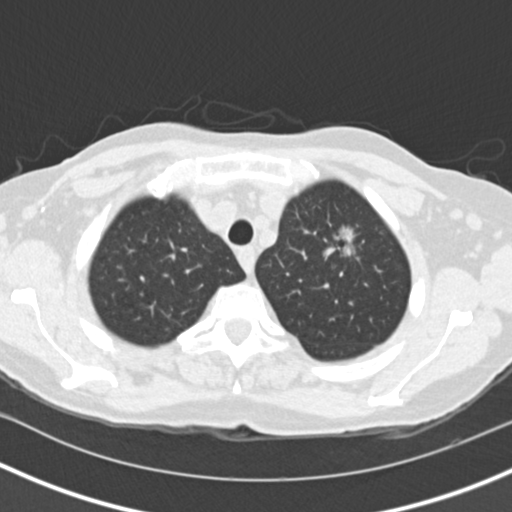
Low-dose screening chest CT, axial slice; first (baseline) screen; lung window (W 1500 / L -600 HU); 2 mm slice thickness; standard (soft-tissue) reconstruction kernel (B30f); slice 25 of 146 in the series; 512 × 512 image matrix. Female participant, aged 73 years at enrolment. Current smoker at enrolment.
Expert-annotated lung lesion, bounding box <311,221,364,283> (left, top, right, bottom; pixels). Reader record for this screening exam (exam-level; its link to the box is not recorded): non-calcified nodule or mass ≥4 mm, left upper lobe, 27 × 21 mm, spiculated (stellate) margins, soft tissue attenuation. Official screen result: positive, change unspecified: nodule(s) >= 4 mm or enlarging nodule(s), mass(es), or other non-specific abnormalities suspicious for lung cancer. Participant outcome: lung cancer diagnosed 72 days after this screen — bronchiolo-alveolar adenocarcinoma, NOS, left upper lobe, moderately differentiated (G2), stage IIIB (AJCC 6th edition), 17 mm at pathology.